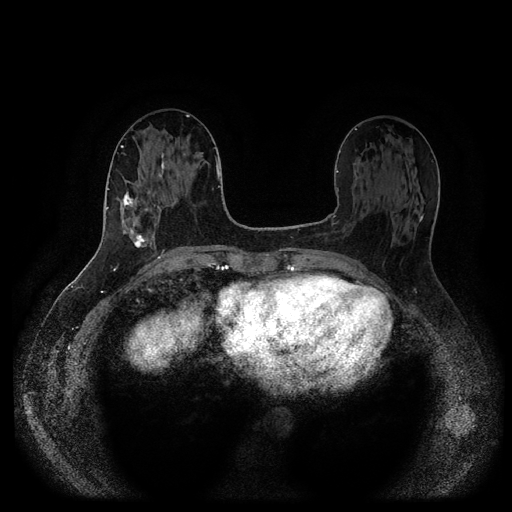
Breast MRI (dynamic contrast-enhanced, multi-phase), one axial slice. Slice 44 of 116 in the series (ordered by position). Dynamic contrast-enhanced series, time point 2 of 5 at this slice position (early post-contrast). 1.5 T. TE 2.6 ms, TR 5.3 ms. 512 × 512 image matrix, field of view 360 × 360 mm. Female patient, age 58 years.
Outlined on this slice (semi-automatic segmentation, software-assisted and operator-edited):
- breast lesion (labelled 'tumour' in the annotation; benign lesions carry a separate 'benign' label): box from (x=122, y=191) to (x=149, y=251) px